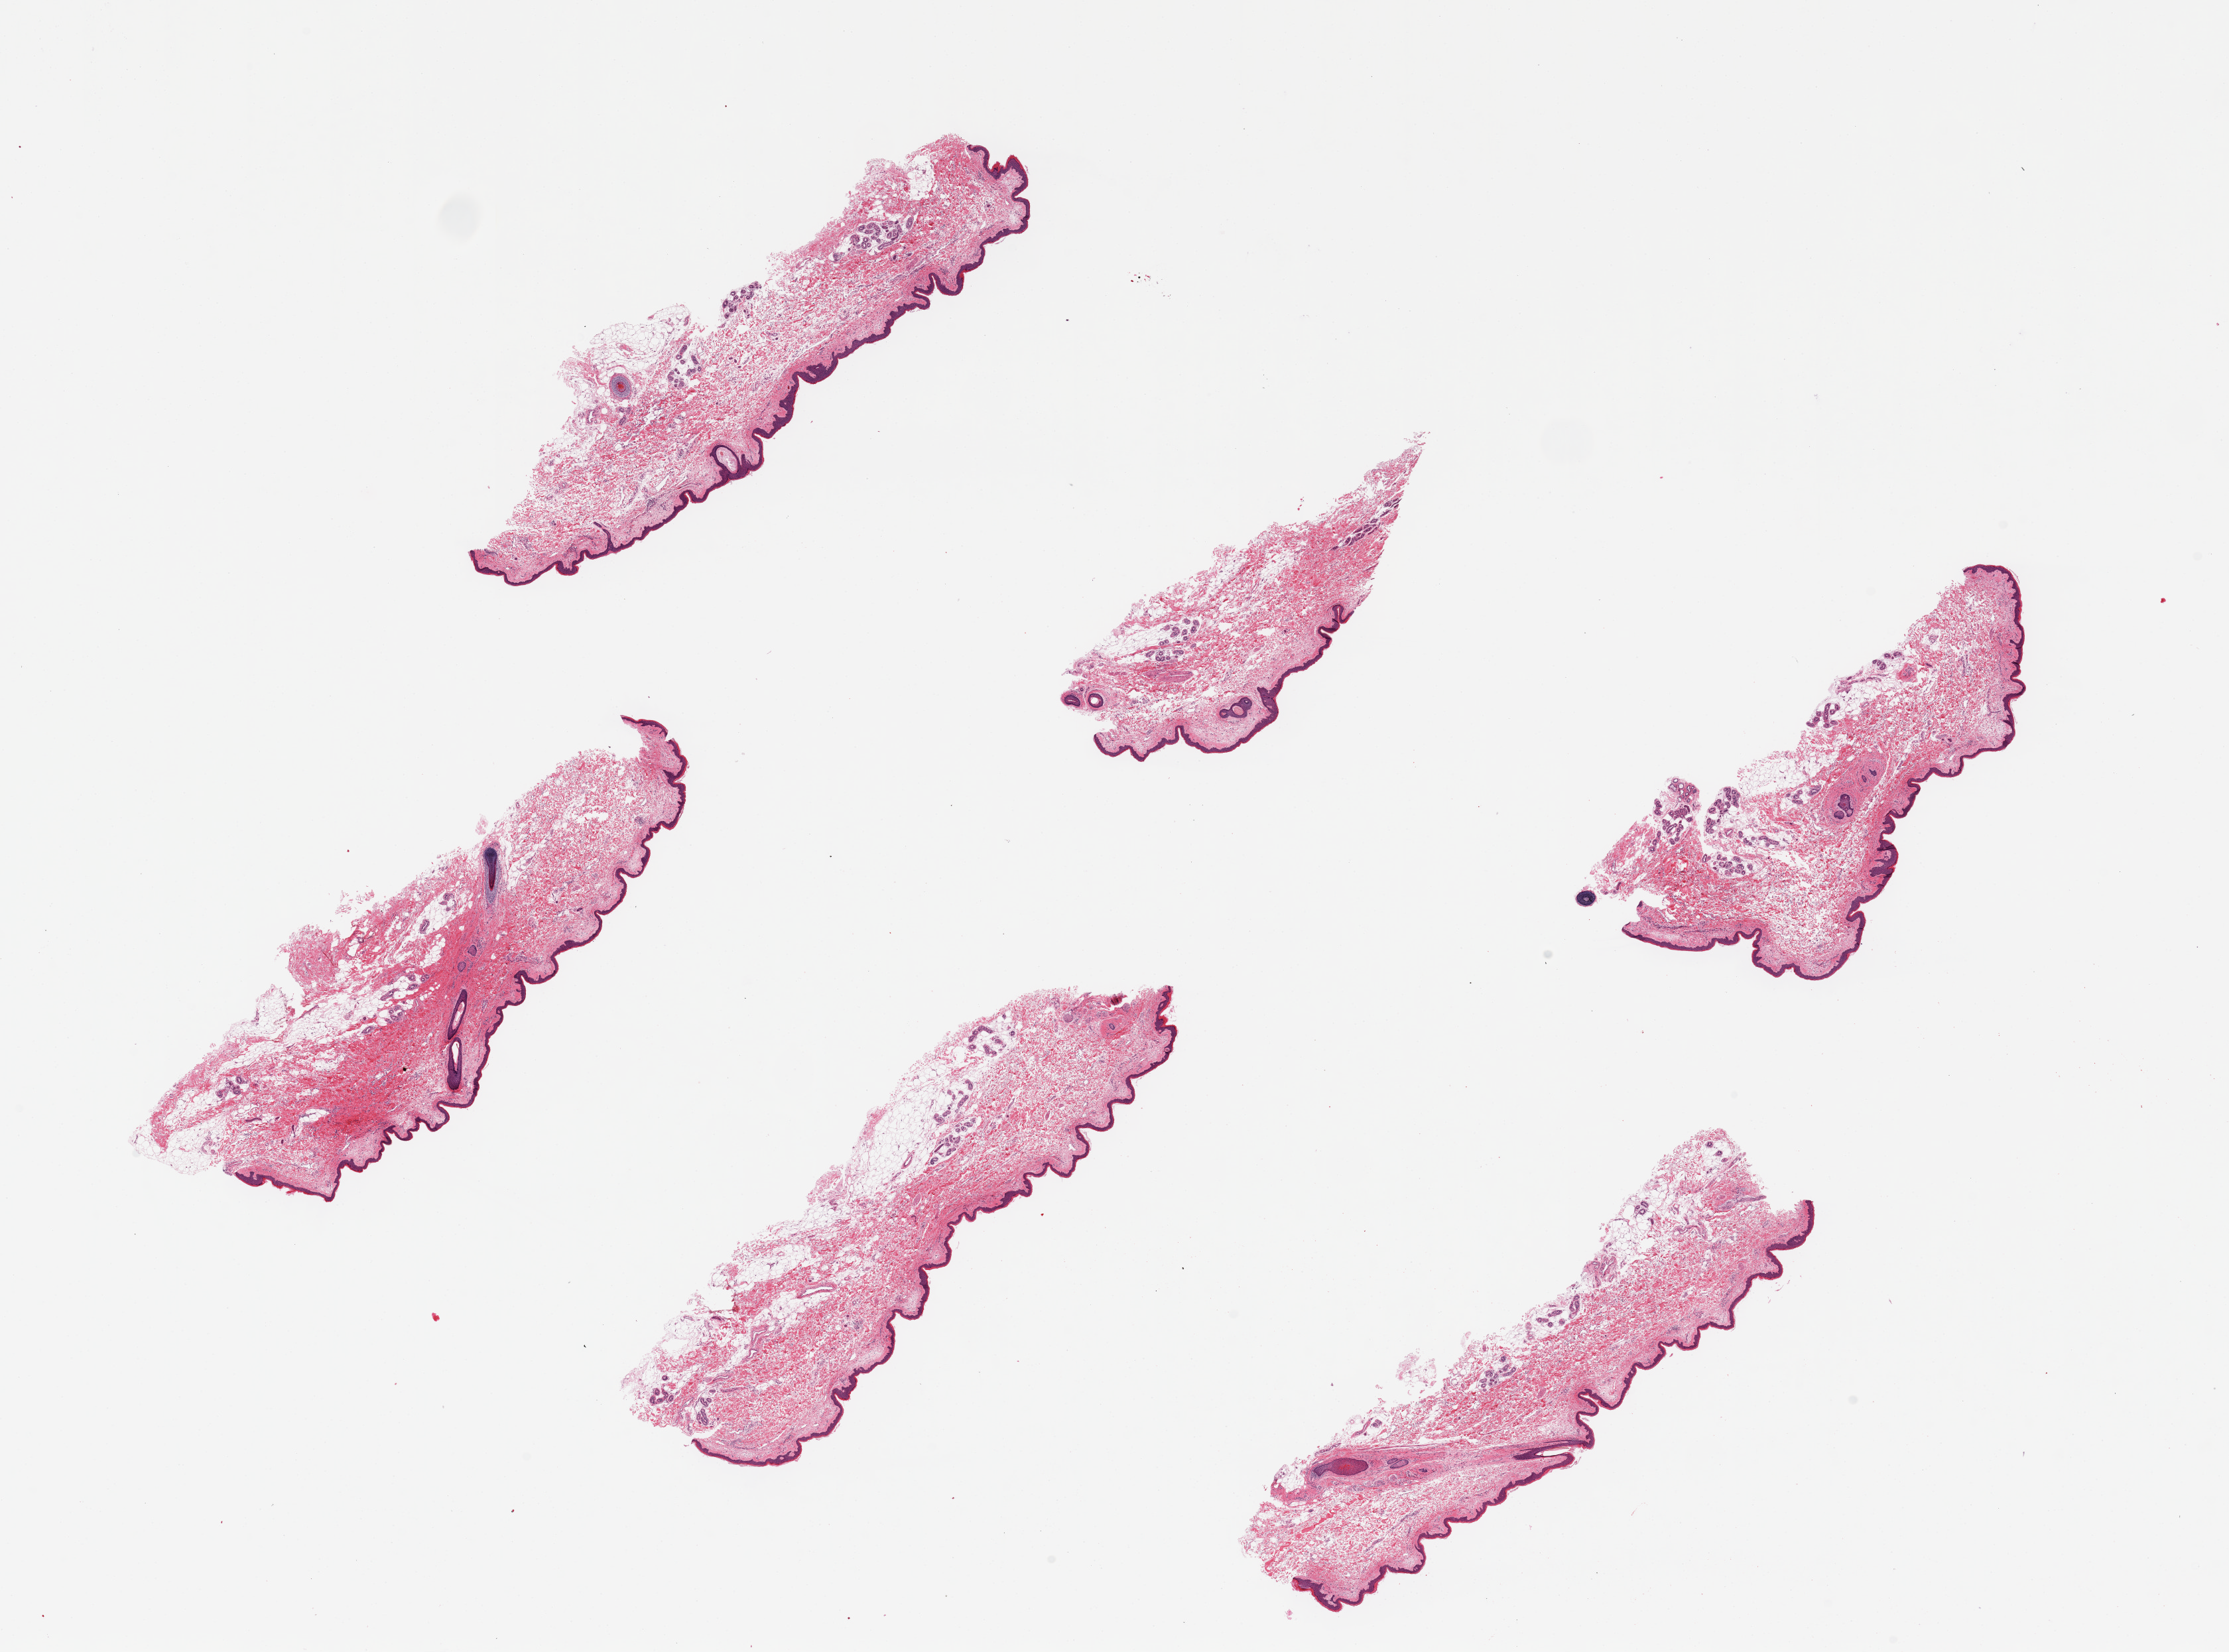
Whole-slide image, hematoxylin and eosin (H&E) stain — whole scanned area (about 26.6 x 19.7 mm, from a 20x scan) shown as a low-resolution overview; PAXgene-fixed paraffin-embedded (PFPE) section; sampled site (target tissue): skin of suprapubic region; donor tissue sample. Donor: female.
Pathologist's review note for this sample: 6 pieces, up to 8x3mm; squamous epithelium is 2-3% thickness.